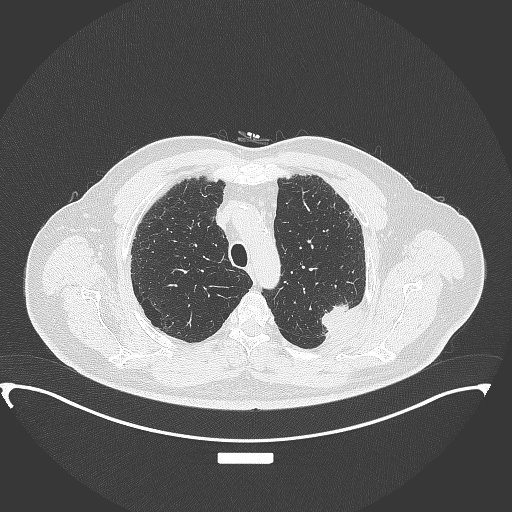
Chest CT, one axial slice; position 282 of 350 along the scan axis; reconstruction kernel B70f; lung window (W 1500 / L -600 HU); 512 × 512 image matrix, field of view 459 × 459 mm. Male patient, age 64 years. From the clinical record (not read from this slice): clinical TNM (as recorded): T1c N1 M1.
Annotated regions visible in this slice (rectangle marked by the reading radiologist):
- lung tumour (recorded histology: adenocarcinoma): box from (x=319, y=297) to (x=363, y=338) px